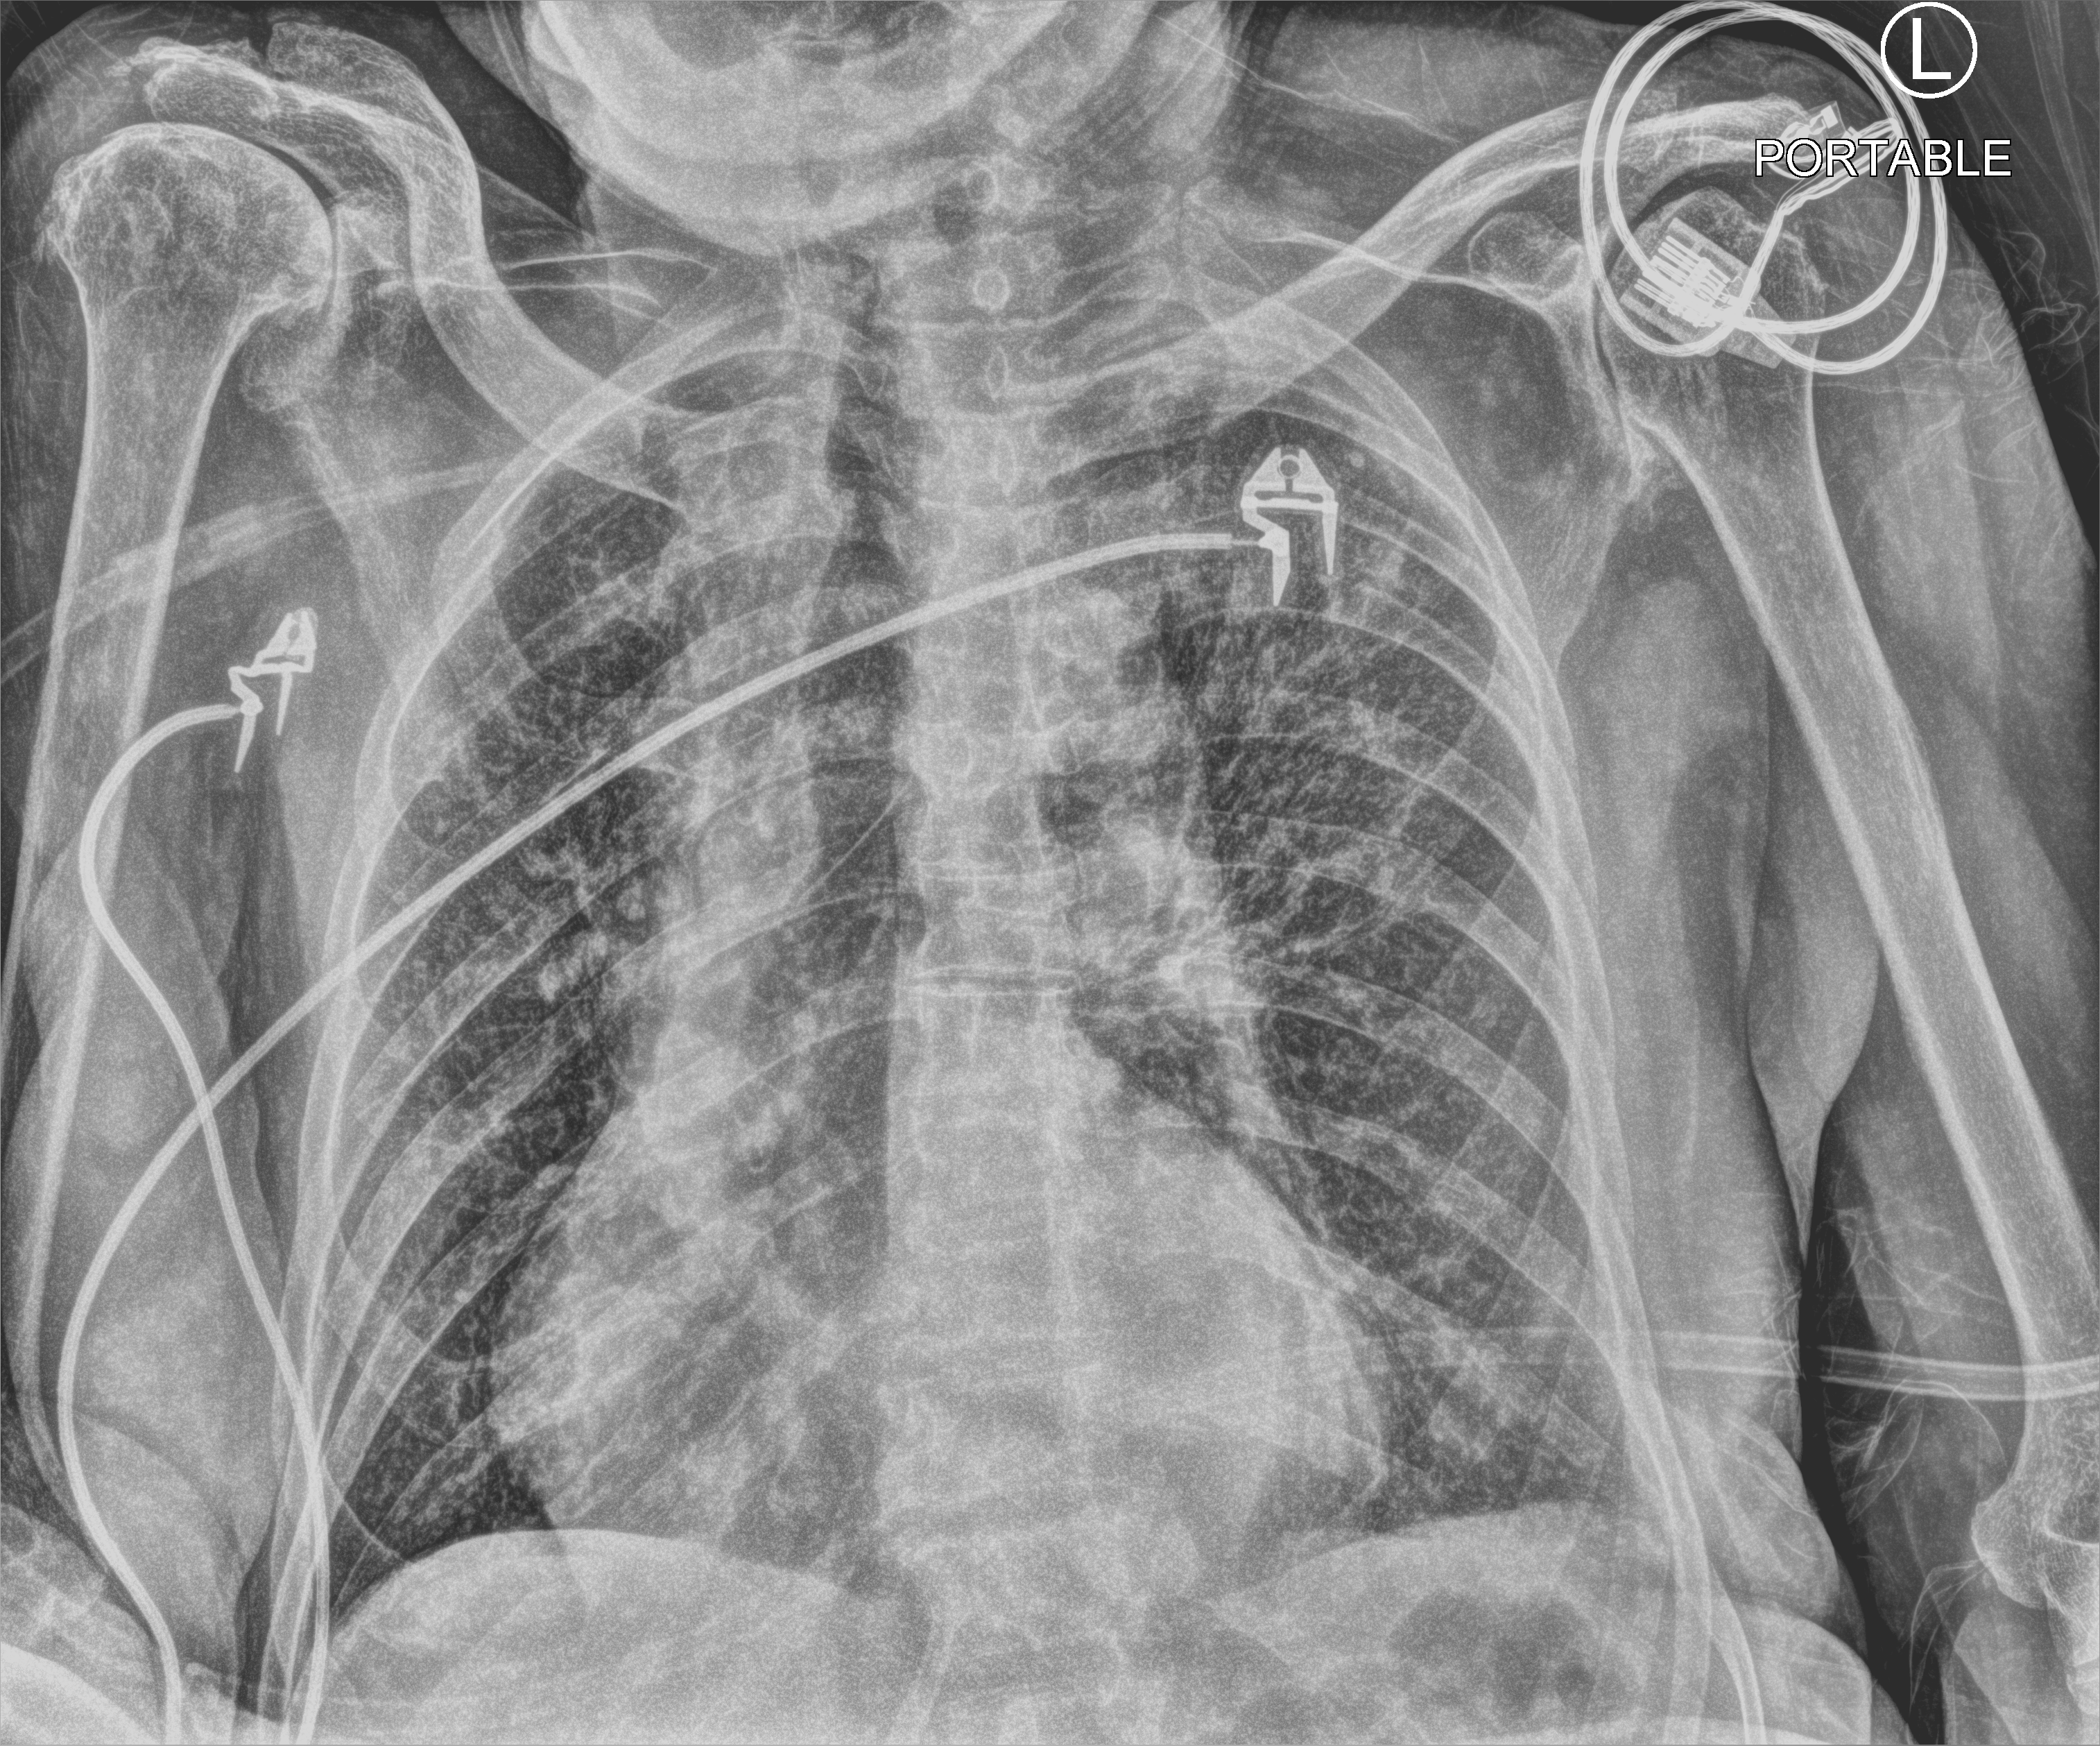
Chest X-ray (portable); anteroposterior (AP) projection. Patient hospitalised with COVID-19; male, aged 75–90 years.
From the hospital-stay record, not from the radiograph (when in the stay this image was taken is not recorded):
- chronic kidney disease (admission record): no
- admitted to intensive care during this hospital stay: no
- mechanically ventilated during this hospital stay: no